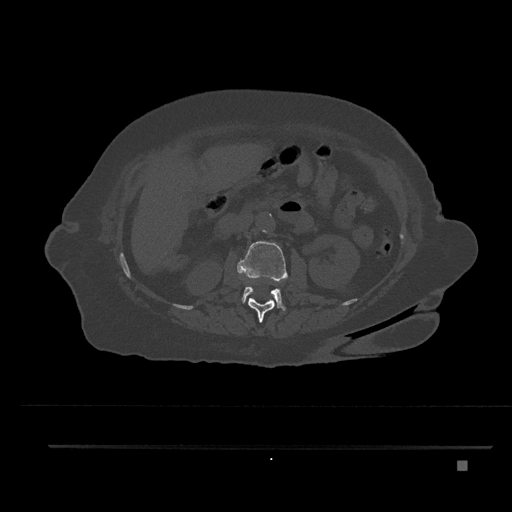
CT including the spine, one axial slice; reconstruction kernel Br40s/3; 120 kVp; bone window (W 1800 / L 400 HU); 0.5 mm slice thickness; 512 × 512 image matrix, field of view 437 × 437 mm. Female patient, age 76 years. Case-level facts recorded for this patient, not image findings: primary cancer: lung; vertebrae with lytic lesions (as recorded): T11, L3.
Outlined on this slice (semi-automatic segmentation, software-assisted and operator-edited):
- L1 vertebra: bounding box [x1, y1, x2, y2] px = [248, 298, 276, 322]
- L2 vertebra: [237, 241, 288, 311]